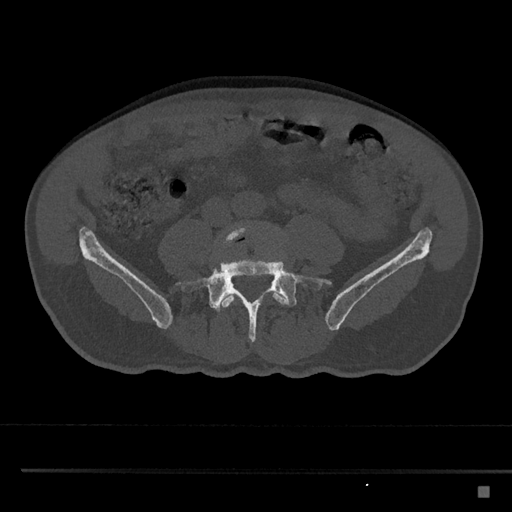
CT including the spine, one axial slice. Slice 600 of 797 in the series (ordered by position). 120 kVp. Bone window (W 1800 / L 400 HU). 0.5 mm slice thickness. 512 × 512 image matrix. Male patient, age 59 years. Case-level facts recorded for this patient, not image findings: primary cancer: prostate.
Structures marked on this image (semi-automatic segmentation, software-assisted and operator-edited):
- L4 vertebra: bounding box <215,224,289,312> (left, top, right, bottom; pixels)
- L5 vertebra: <177,252,331,343>